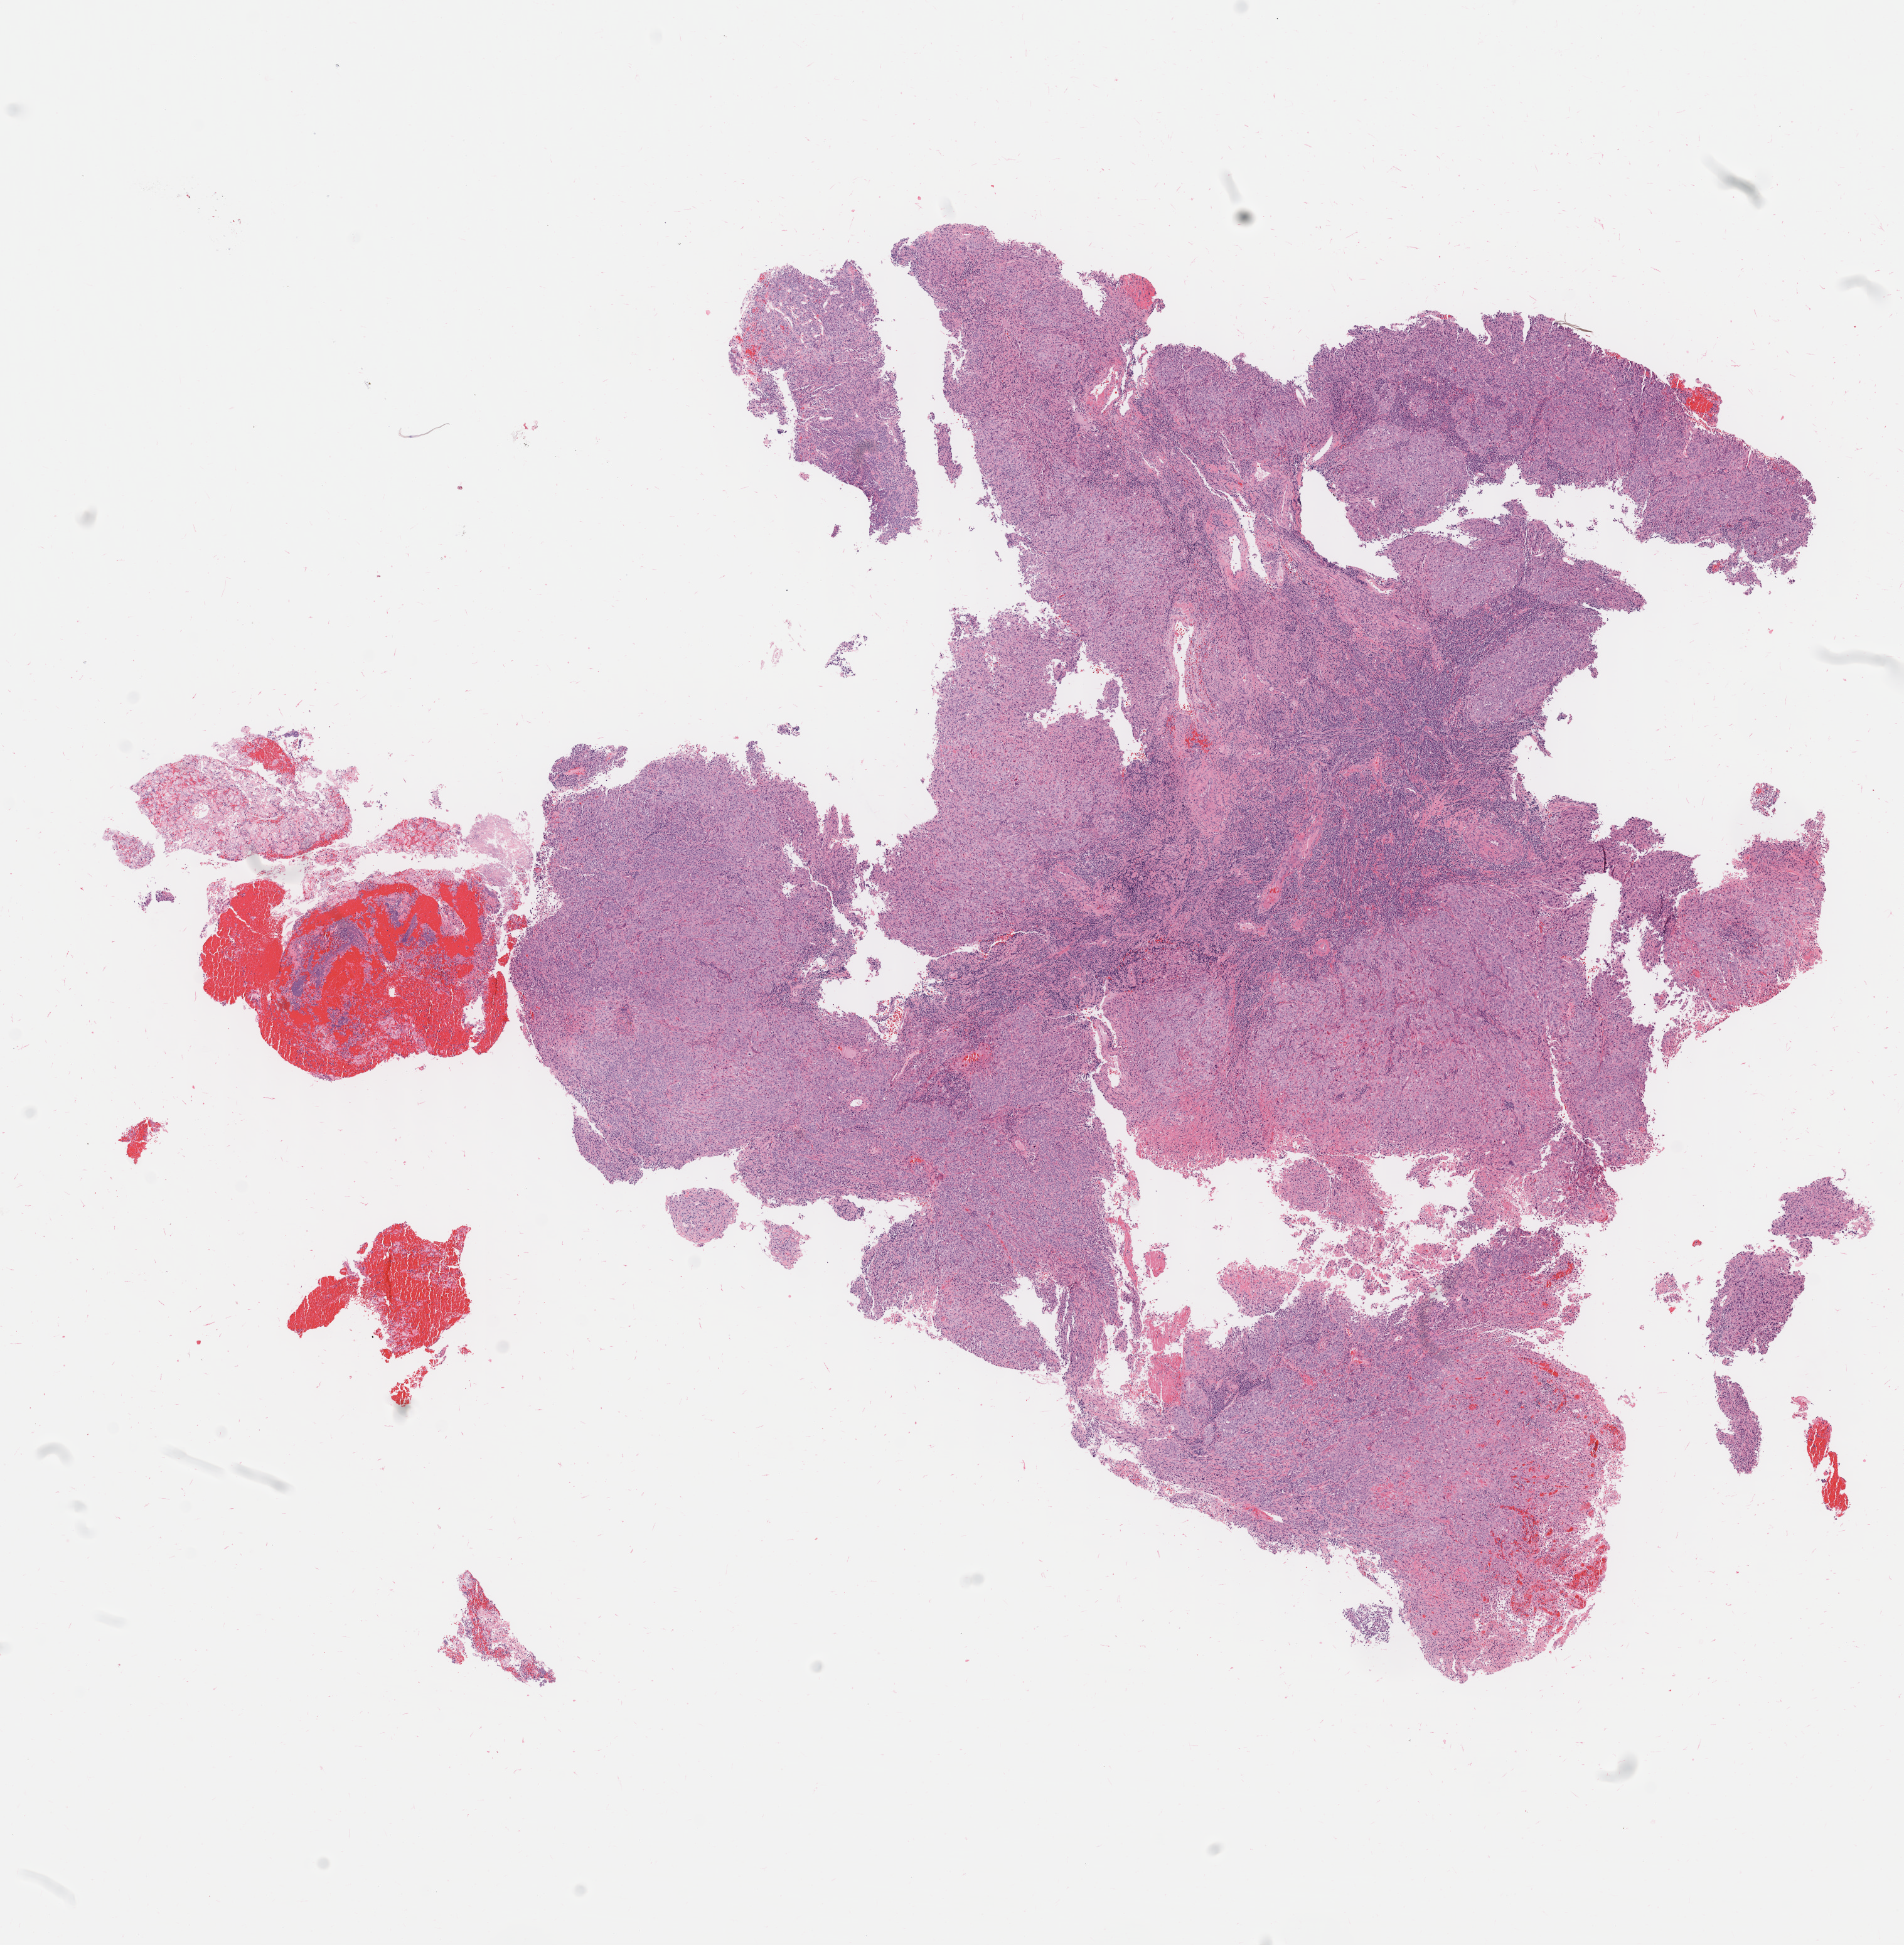
Haematoxylin and eosin whole-slide image, whole scanned area (about 12.1 x 12.3 mm) shown as a low-resolution overview. Tumor tissue. Anatomic site: cervix. Female patient, 32 years old.
Diagnosis: Squamous cell carcinoma, large cell, nonkeratinizing, NOS.